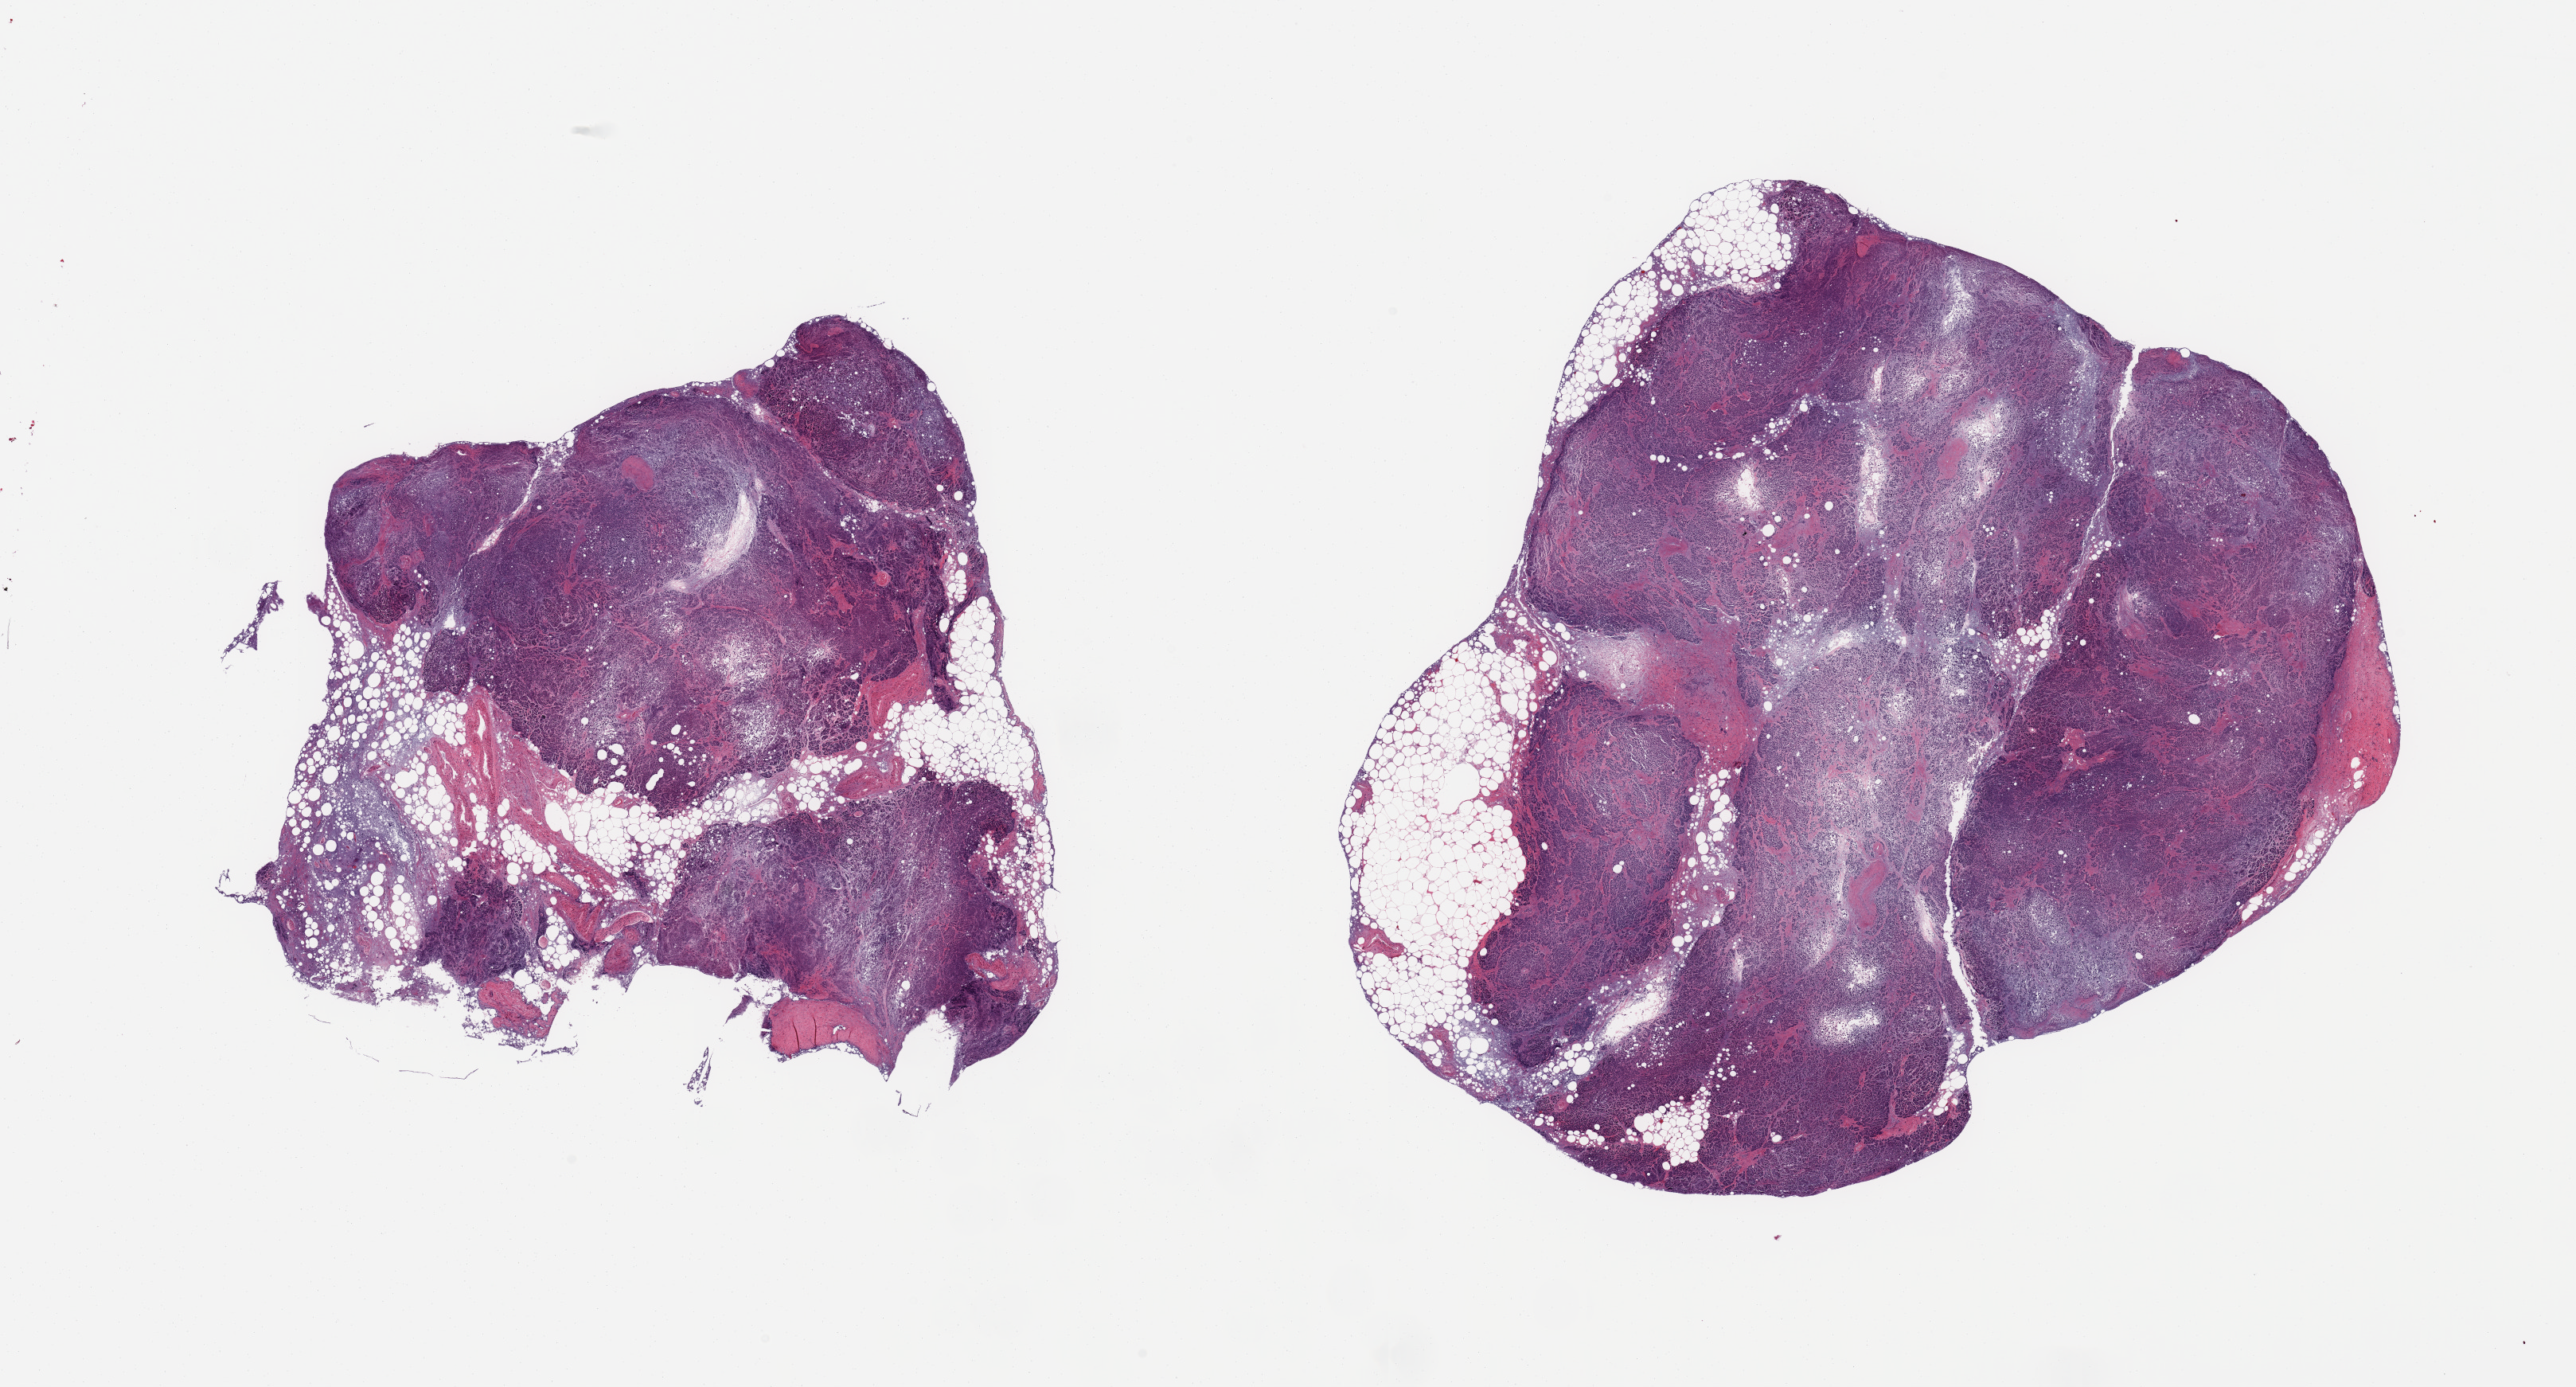
Hematoxylin and eosin (H&E) whole-slide image, brightfield — low-resolution overview of the scanned area, about 25.6 x 13.8 mm; PAXgene-fixed paraffin-embedded (PFPE) section; sampled site (target tissue): pancreas; tissue donor sample. Male donor.
Review note (as recorded): 2 pieces; excessive autolysis; most areas not recognizable.